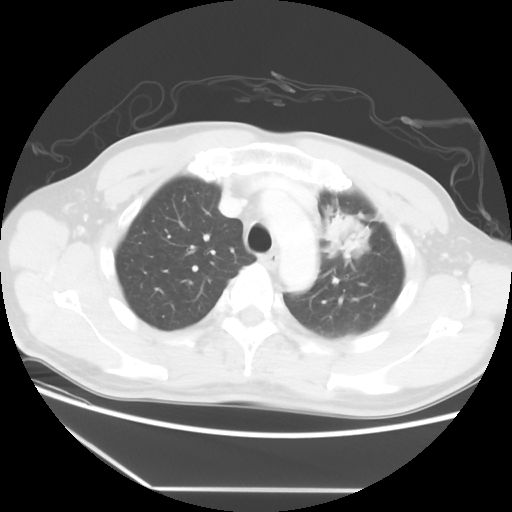
Chest CT, one axial slice. Position 43 of 56 along the scan axis. Reconstruction kernel STANDARD. 120 kVp. Lung window (W 1500 / L -600 HU). 512 × 512 image matrix. Patient: male, 53 years. Case-level facts recorded for this patient, not image findings: clinical TNM (as recorded): T2a N1 M1b.
Structures marked on this image (bounding box drawn by a radiologist):
- lung tumour (recorded histology: adenocarcinoma): bounding box [x1, y1, x2, y2] px = [325, 206, 373, 259]